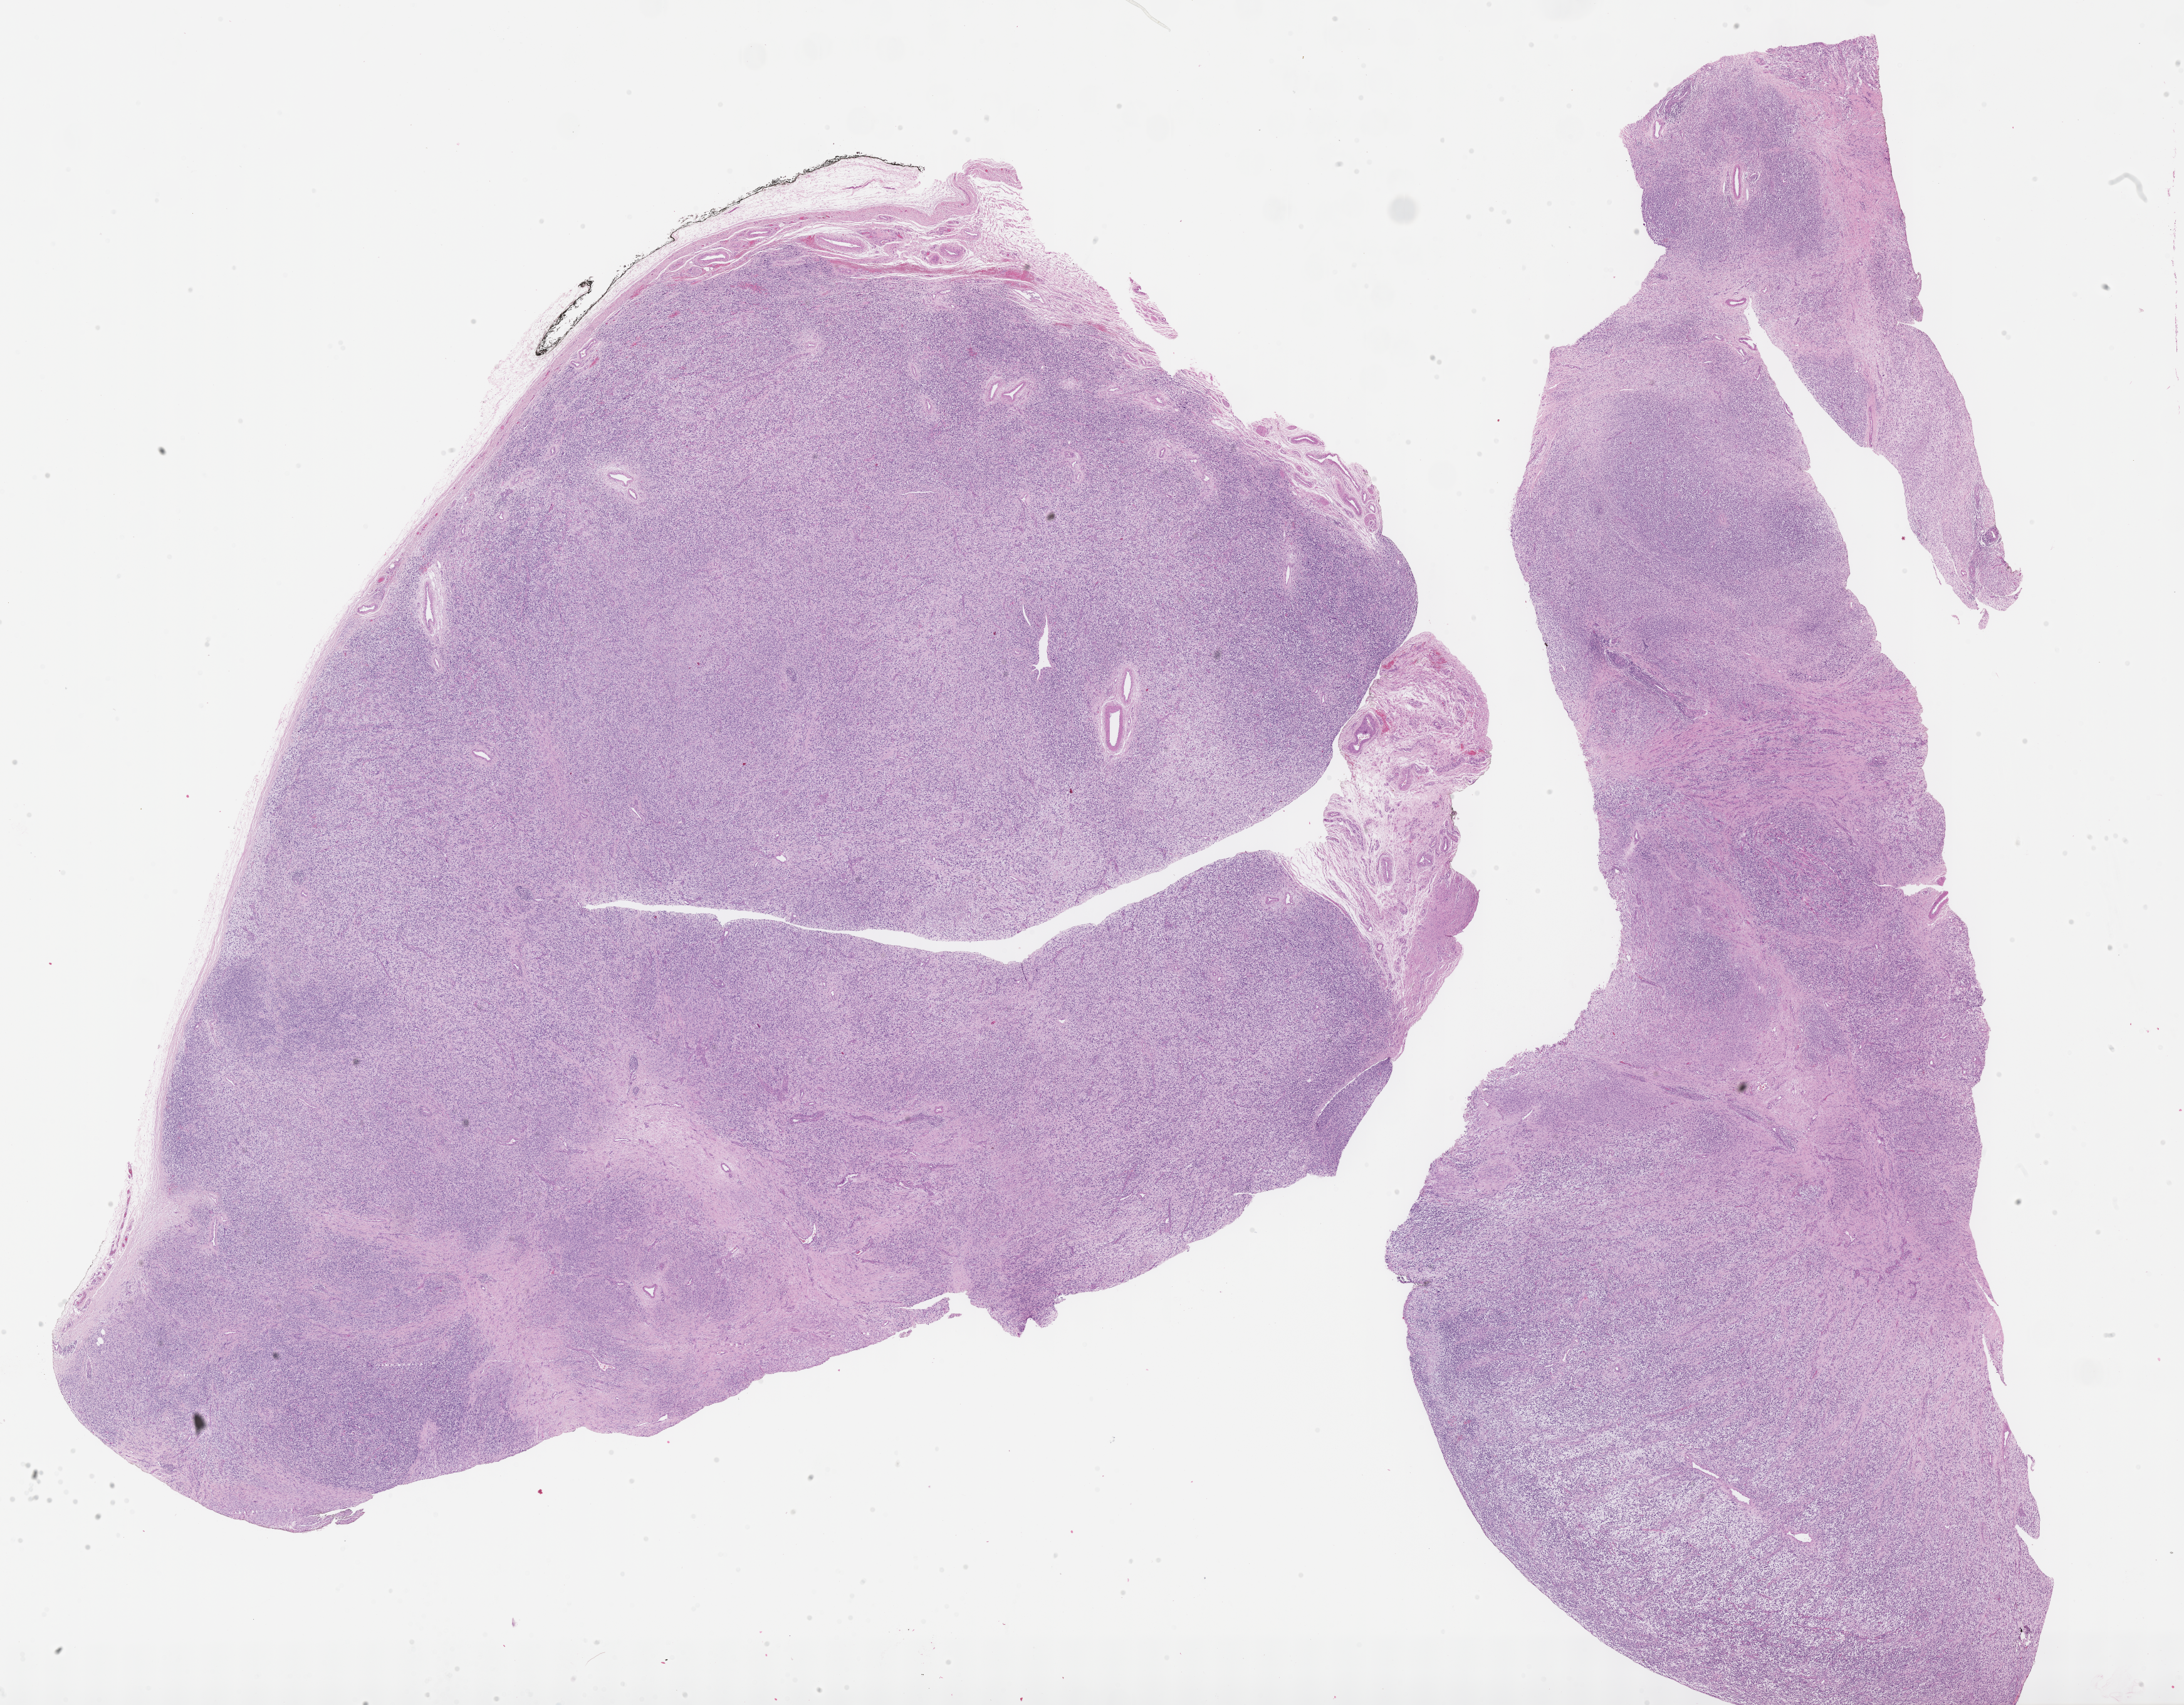
Whole-slide image, haematoxylin and eosin stain of tumor tissue — low-resolution overview of the scanned area, about 28.2 x 22.0 mm. Formalin-fixed, paraffin-embedded (FFPE) tissue. Site: testis, left. Patient: male, age 5.5 years at diagnosis.
Diagnosis: rhabdomyosarcoma; histological classification: spindle cell rhabdomyosarcoma. Stage (as recorded): 1.